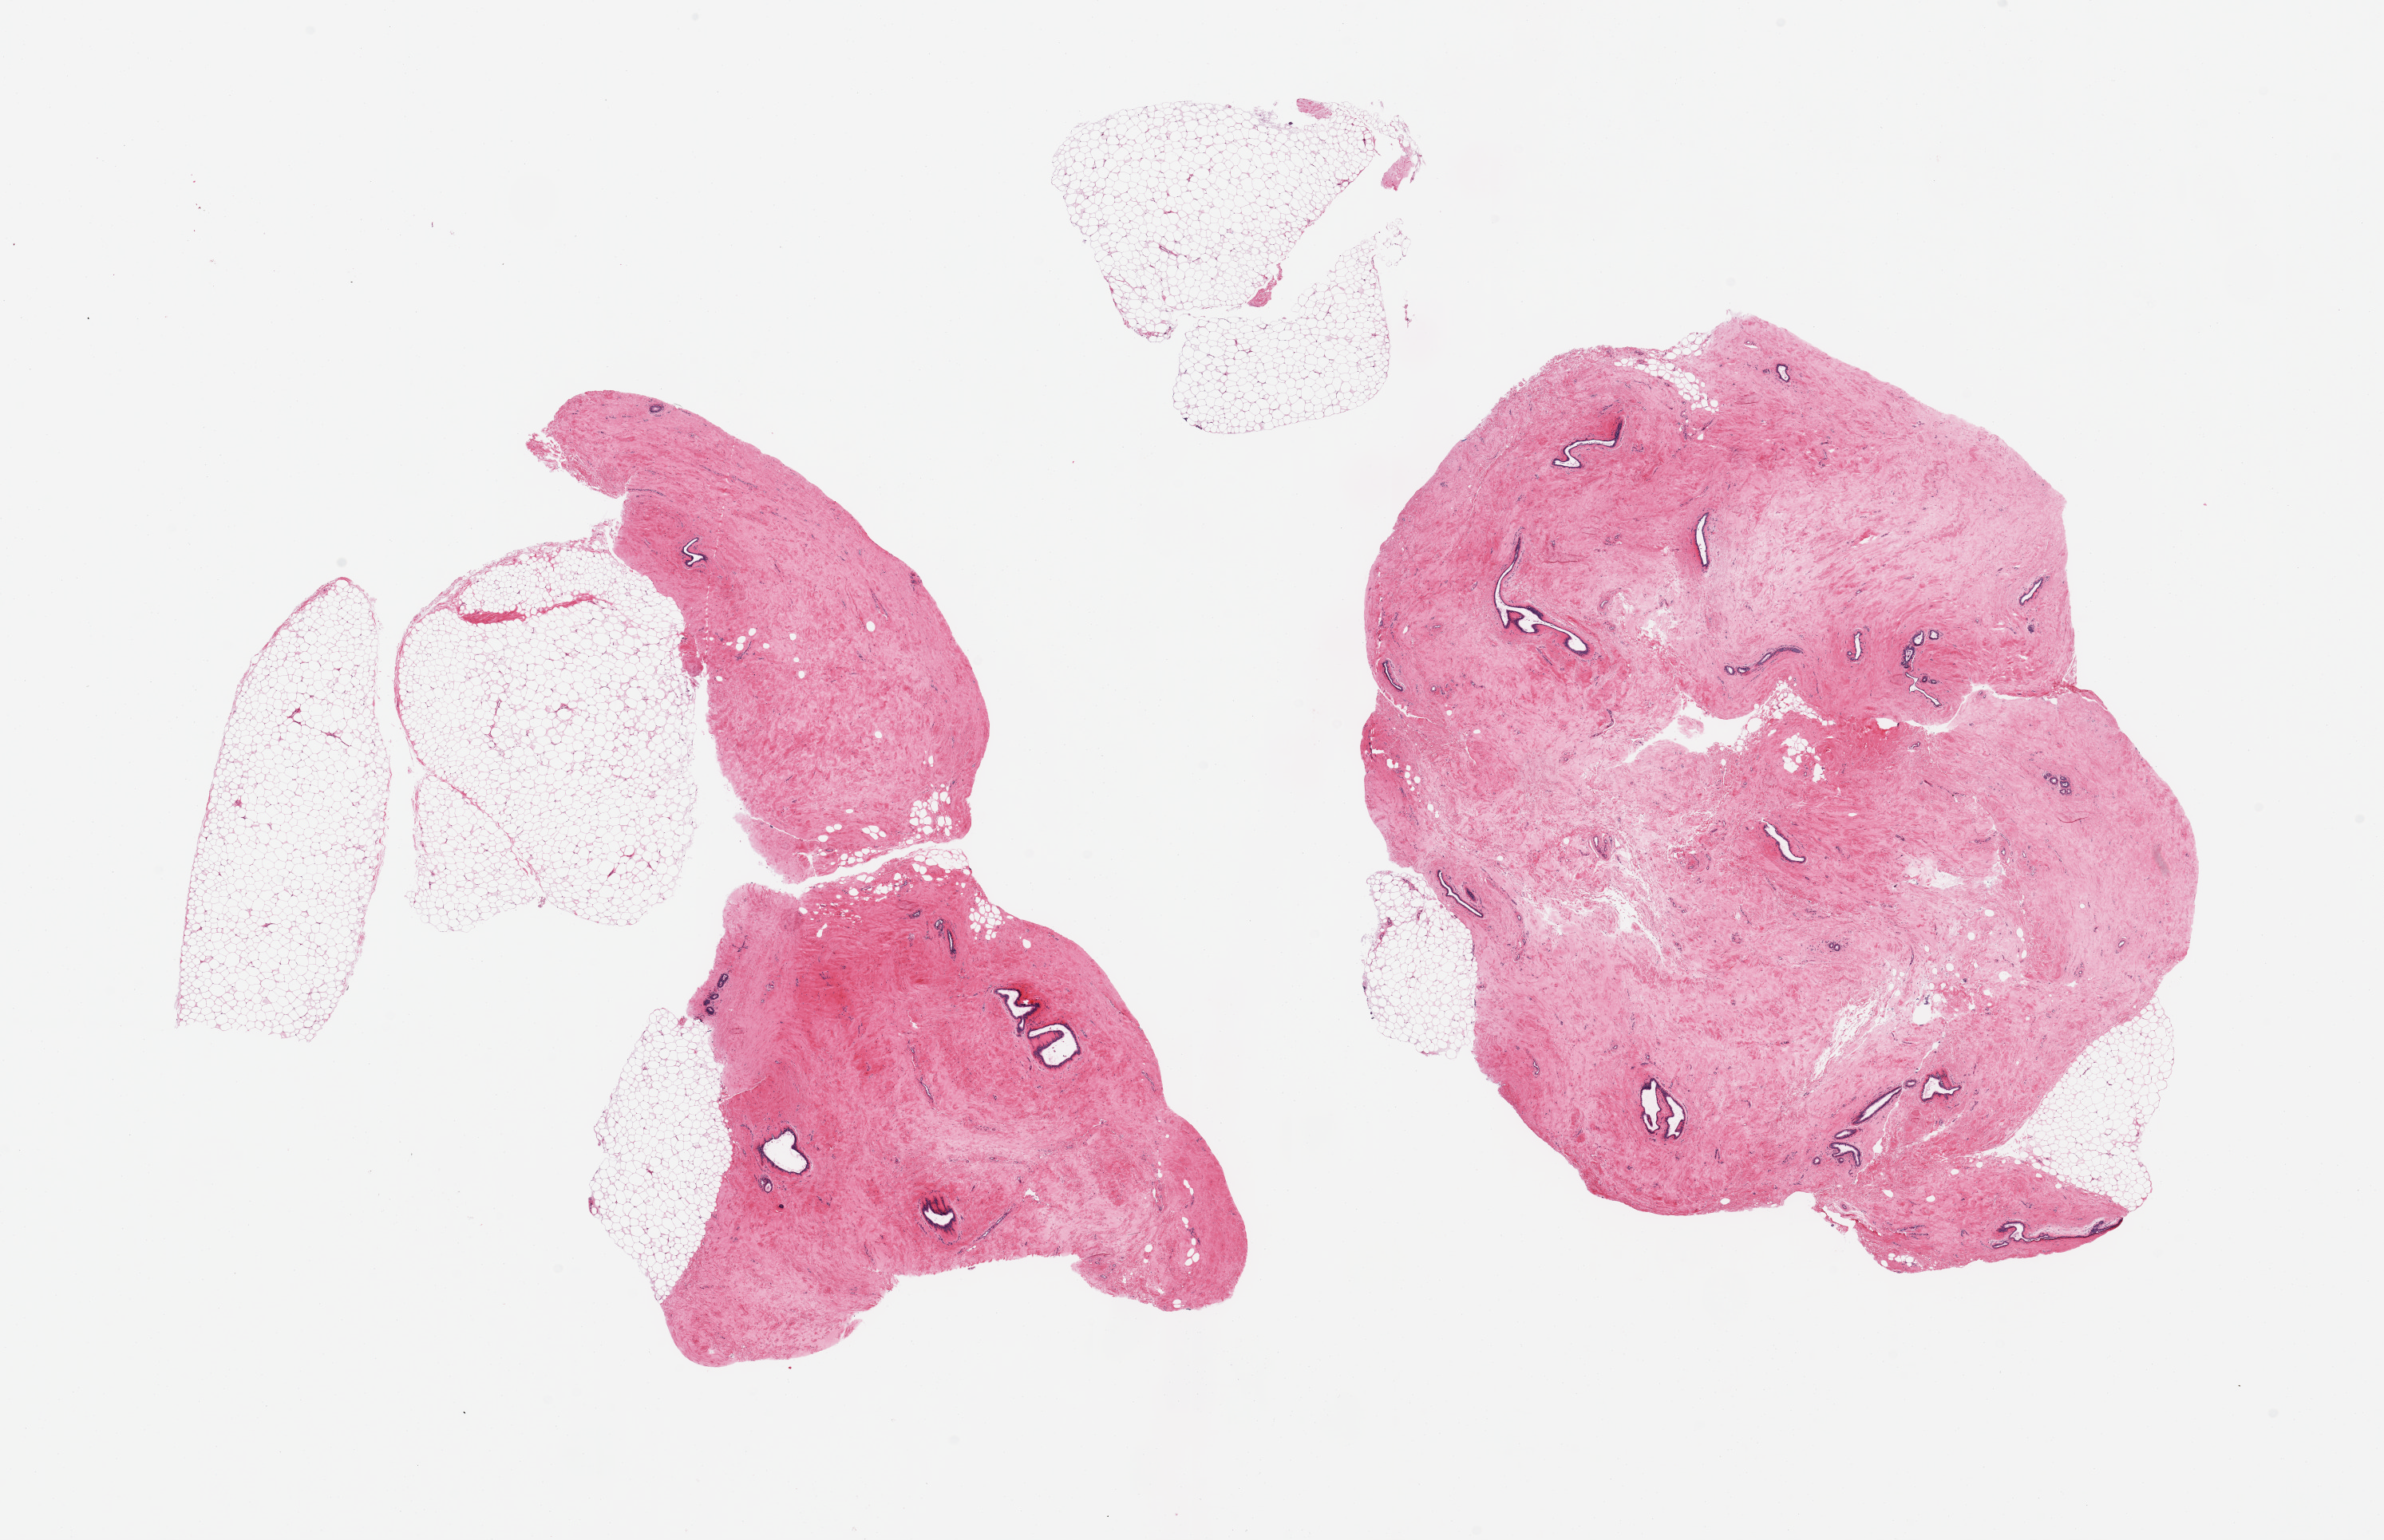
H&E whole-slide image, a low-resolution overview of the entire scanned area, about 23.6 x 15.3 mm (acquisition: 20x scan). PAXgene-fixed paraffin-embedded (PFPE) section. Section of breast (target tissue). Tissue donor sample. Male donor.
* pathologist's review note for this sample: 3 pieces (fragmented); lesser component of fat with dense stroma with scattered dilated ducts consistent with gynecomastia